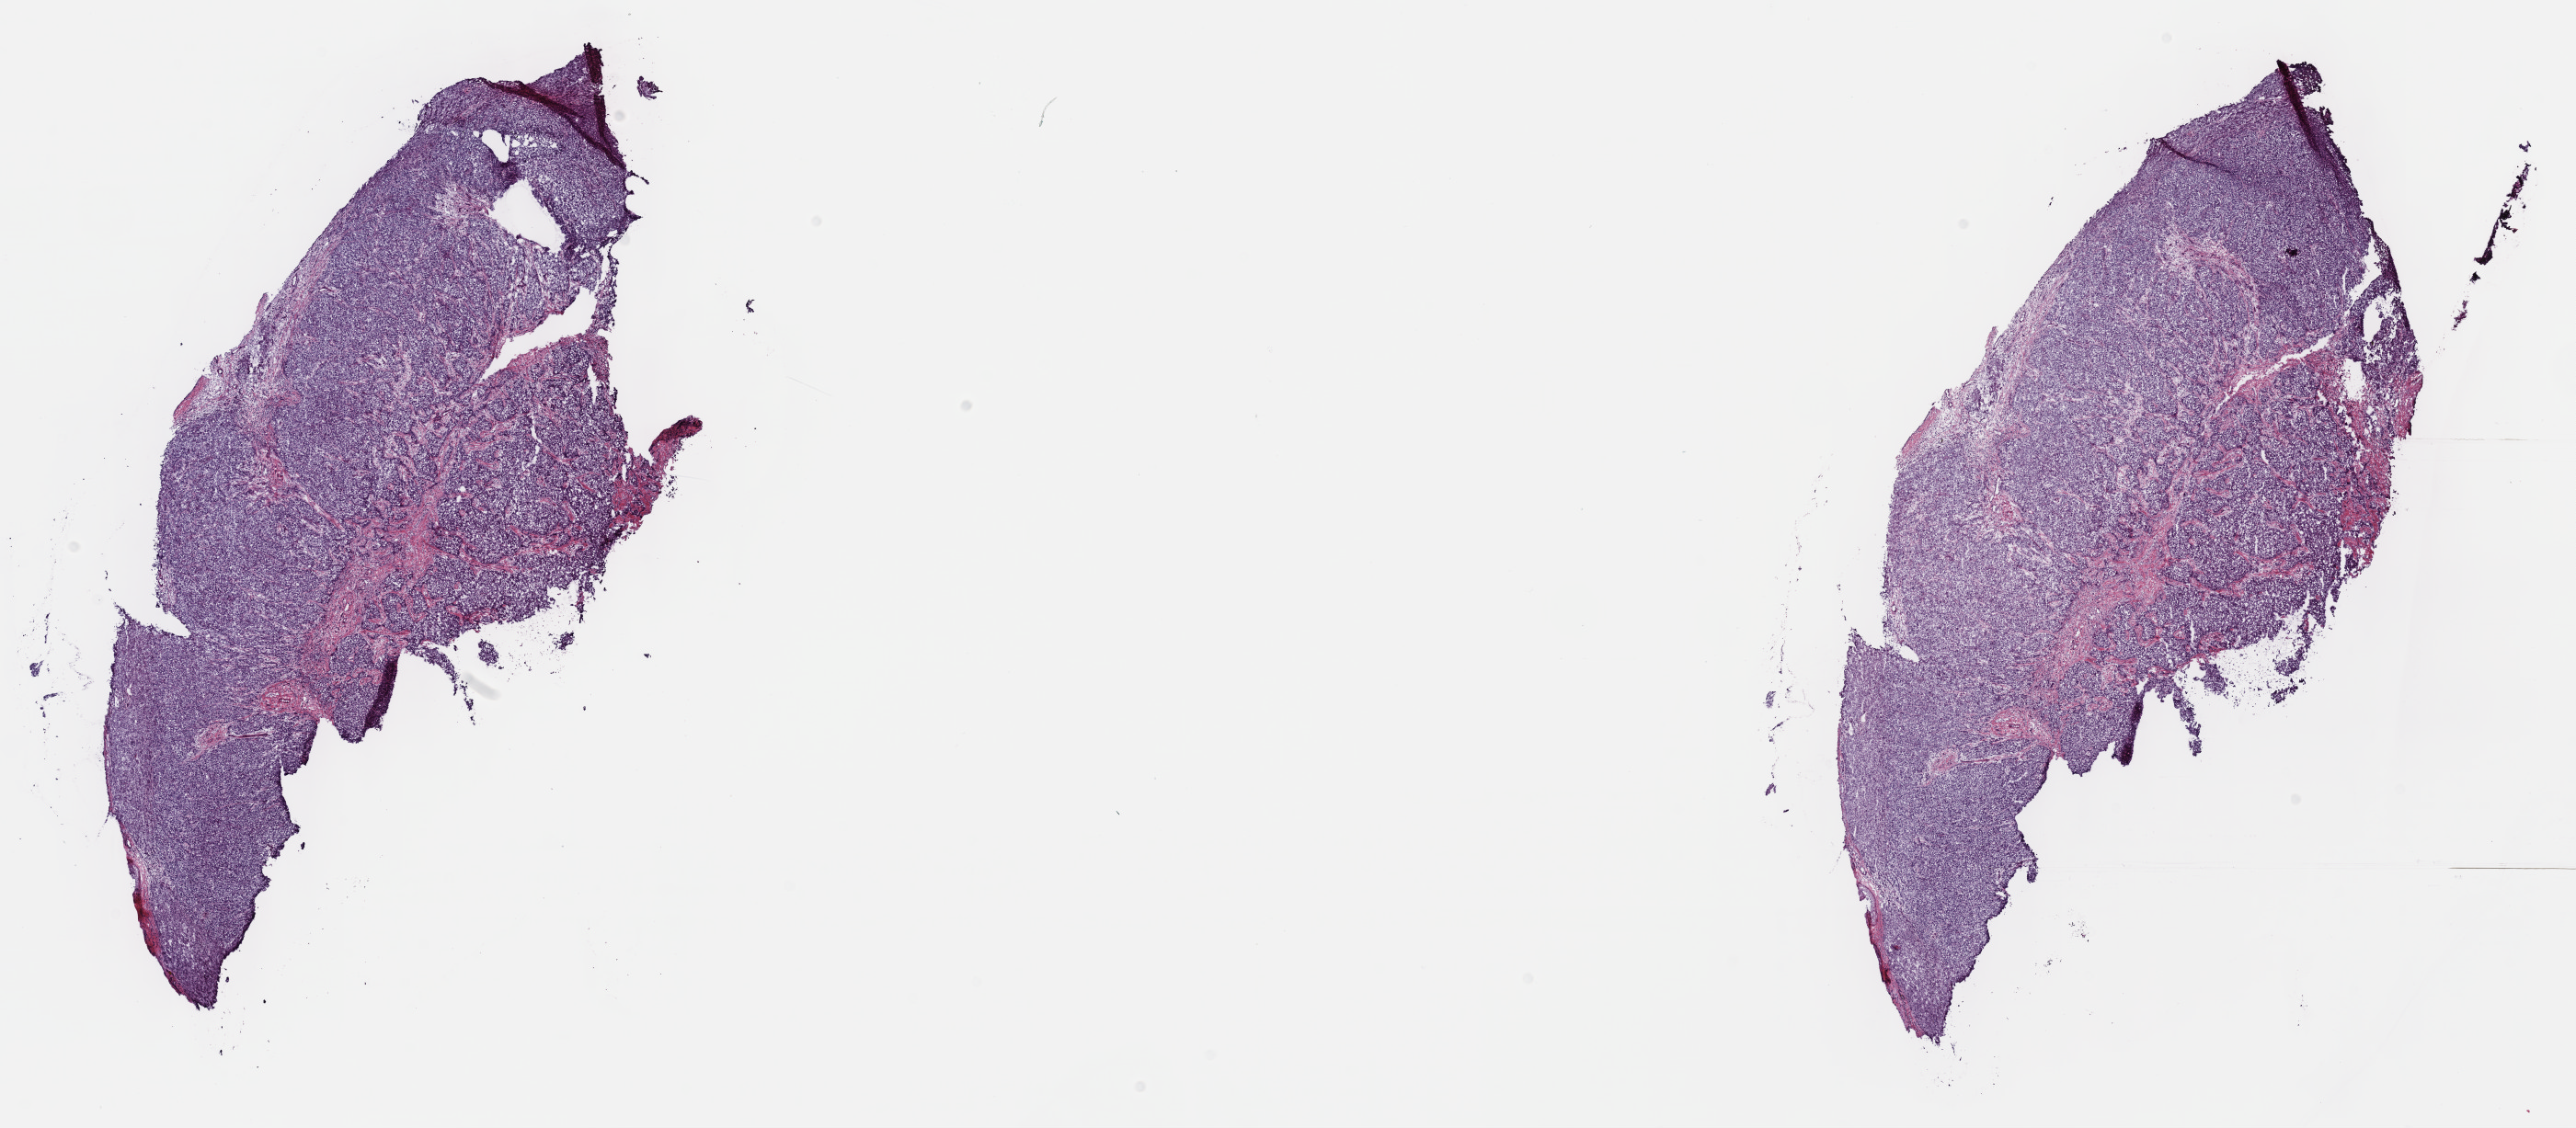
Whole-slide histology image, H&E — low-resolution overview of the scanned area, about 22.7 x 9.9 mm (acquisition: 40x scan). Frozen section from the top of the tissue portion. Liver, primary tumour sample. Male, age 60 years at initial diagnosis. Histologic grade: G2 (moderately differentiated). Pathologist review of this section (percent, as recorded): tumour cells 100%, tumour nuclei 70%, normal cells 0%, stromal cells 0%, necrosis 0%. Inflammatory infiltration, as recorded: lymphocyte infiltration 2%, monocyte infiltration 0%, neutrophil infiltration 0%.
Diagnosis: Hepatocellular carcinoma, NOS. AJCC pathologic stage: II (7th edition).